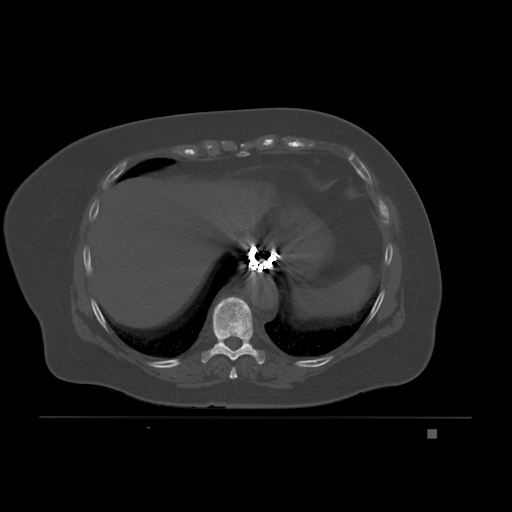
CT including the spine, one axial slice; position 109 of 221 along the scan axis; bone window (W 1800 / L 400 HU); 3 mm slice thickness; 512 × 512 image matrix. Female patient, age 63 years. Case-level facts recorded for this patient, not image findings: primary cancer: breast.
Structures marked on this image (semi-automatically segmented with operator editing):
- T8 vertebra: bounding box <229,367,238,379> (left, top, right, bottom; pixels)
- T9 vertebra: <201,296,266,364>